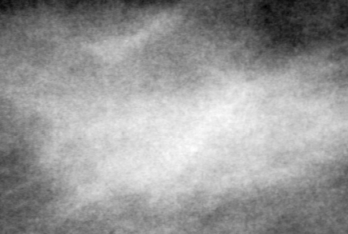
Cropped region of a digitized screen-film mammogram centred on a radiologist-marked abnormality; left breast; MLO view.
Mass, shape irregular, margins spiculated; BI-RADS assessment category 5; pathology (as recorded): malignant.